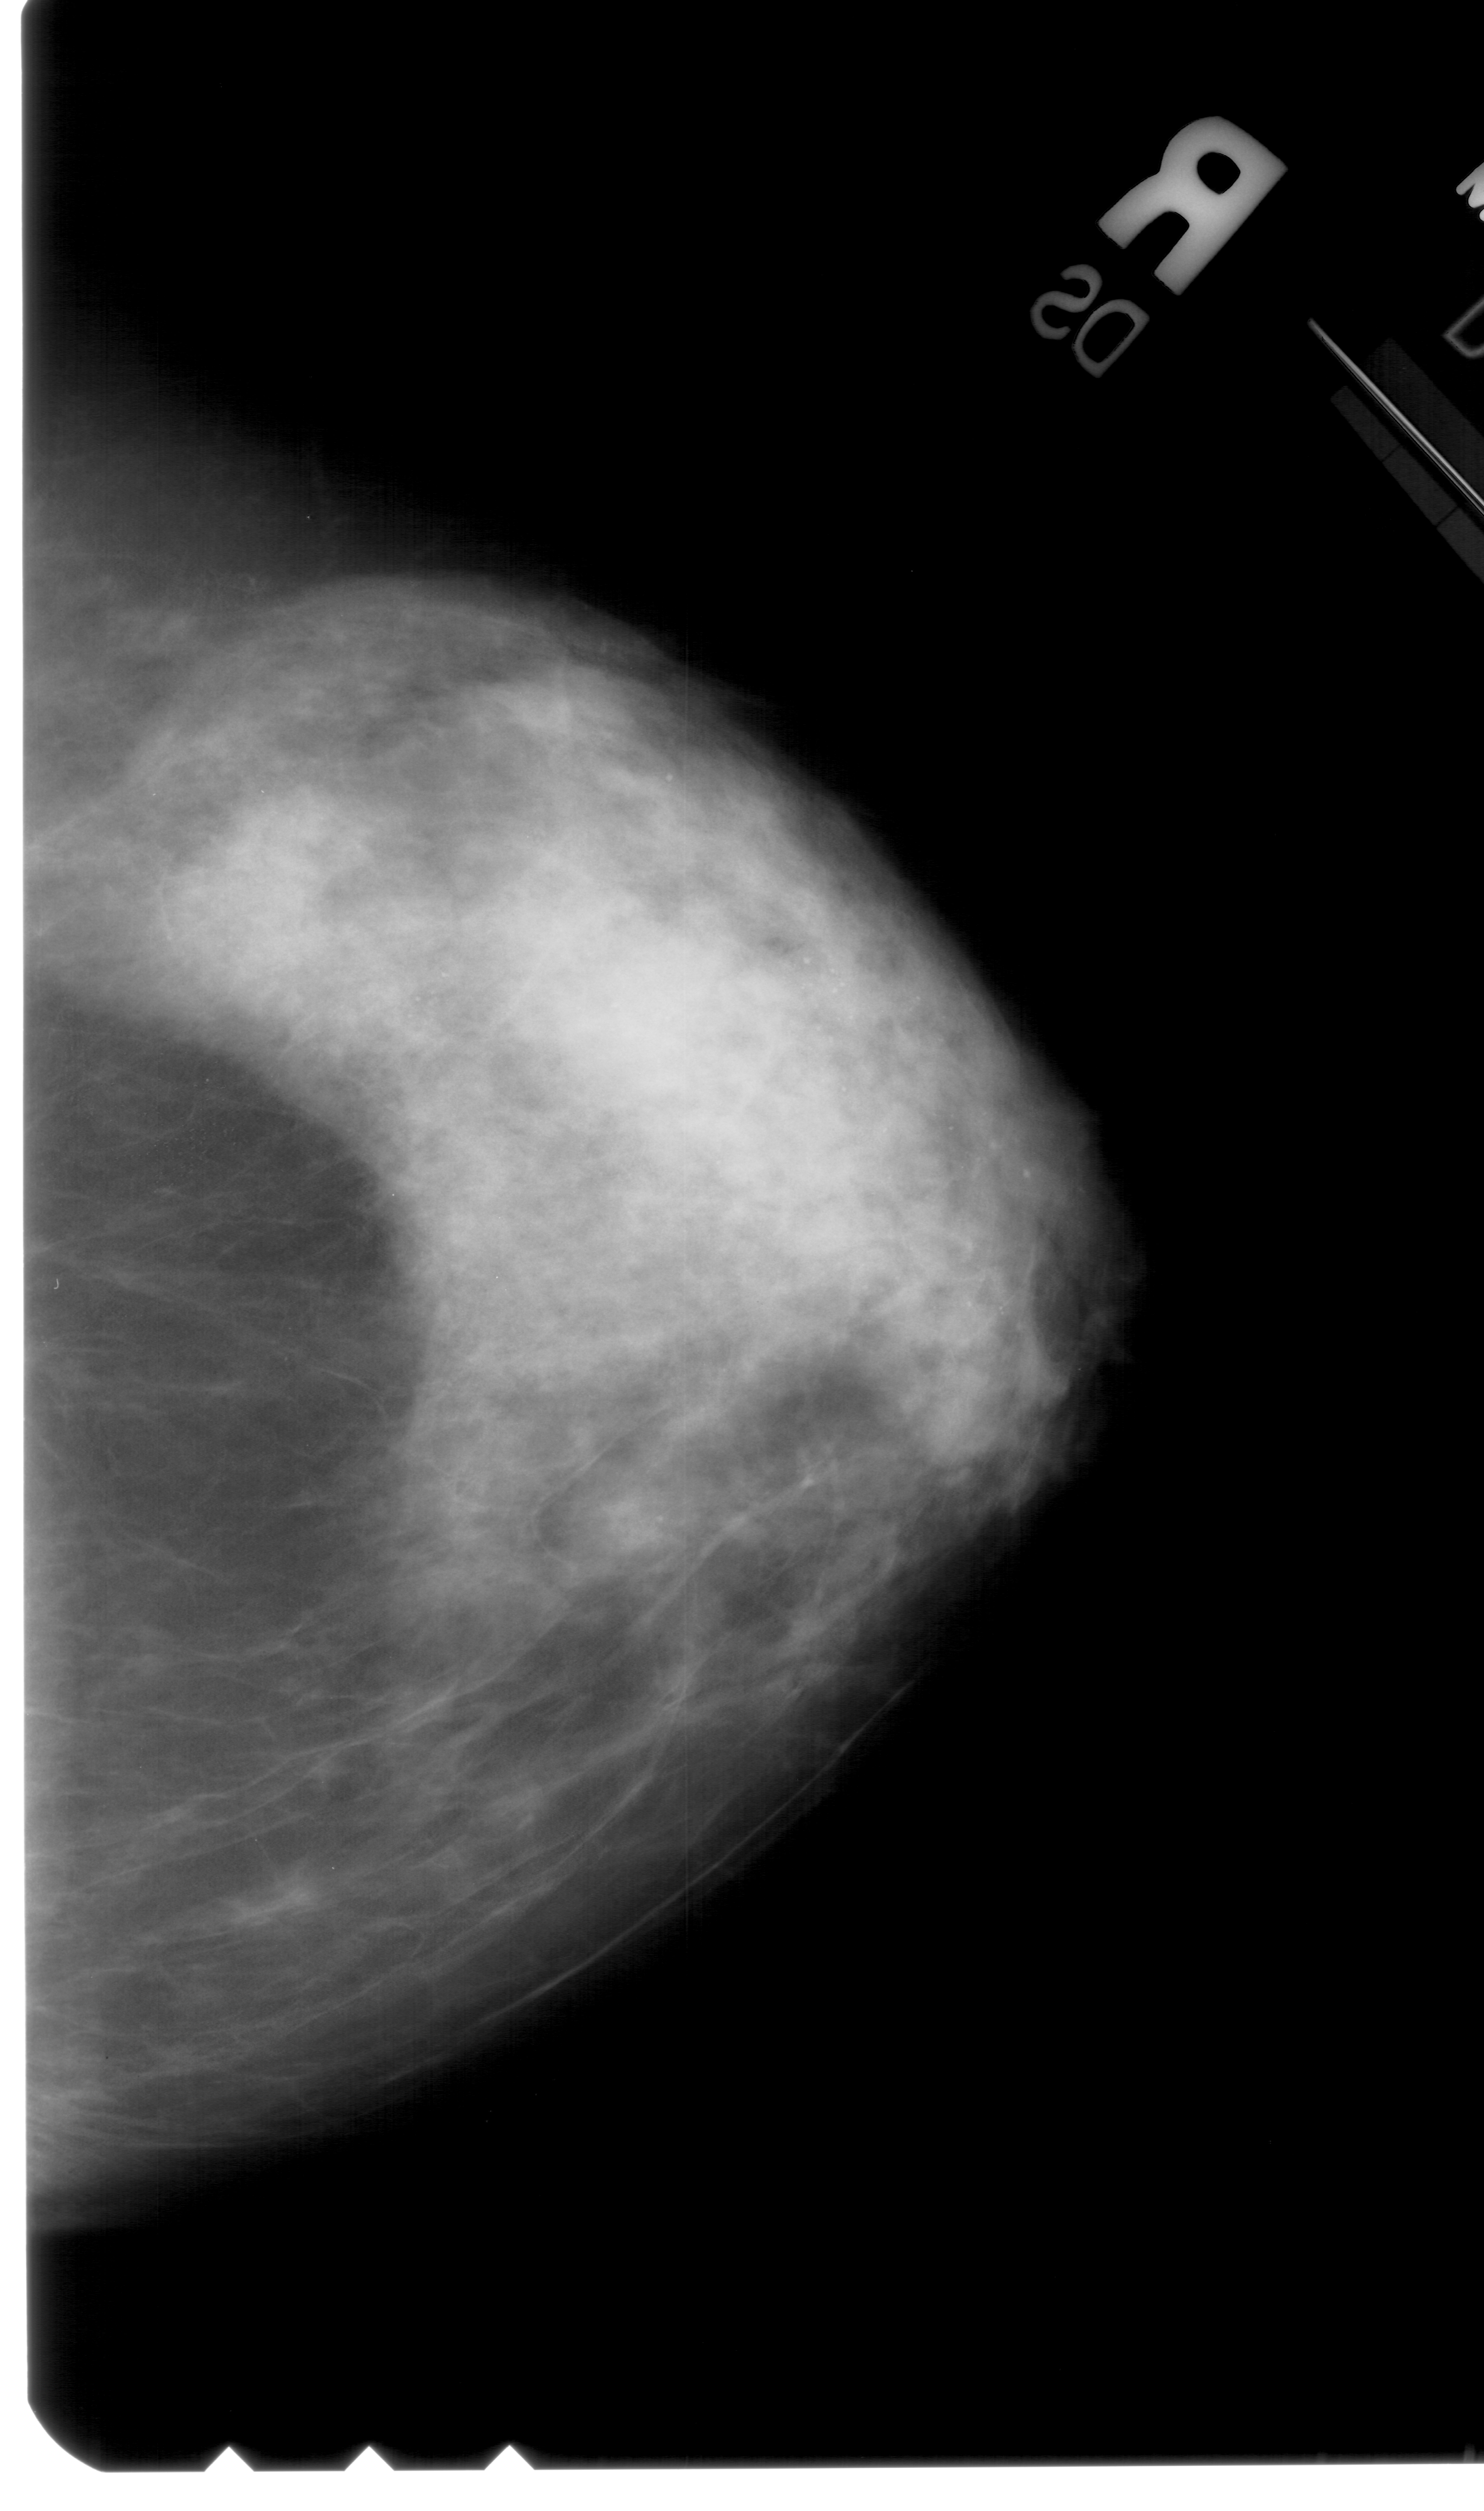
Scanned film-screen mammogram; right breast; CC view; 1484 × 2511 image matrix.
Marked abnormalities (boxes around the expert regions of interest):
- calcifications, morphology amorphous, distribution segmental; BI-RADS assessment category 4; subtlety rating 3 on a 1 (subtle) to 5 (obvious) scale; pathology (as recorded): benign: bounding box (x1, y1, x2, y2) in pixels: (170, 786, 1090, 1361)